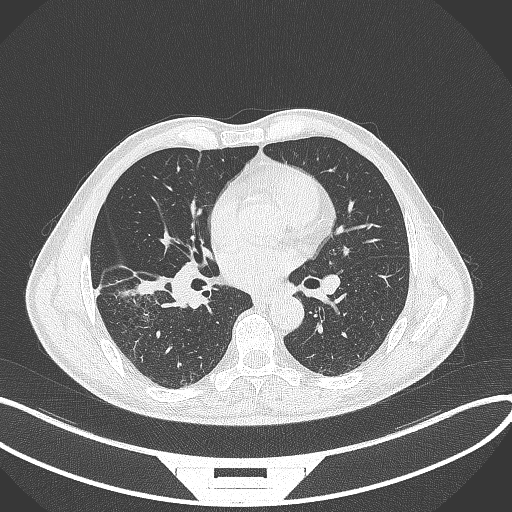
Chest CT, one axial slice; reconstruction kernel B70f; lung window (W 1500 / L -600 HU); 512 × 512 image matrix, field of view 400 × 400 mm. Male patient, age 58 years. Case-level facts recorded for this patient, not image findings: clinical TNM (as recorded): T3 N0 M0.
Outlined on this slice (bounding box drawn by a radiologist):
- lung tumour (recorded histology: squamous cell carcinoma): bounding box <133,275,168,297> (left, top, right, bottom; pixels)